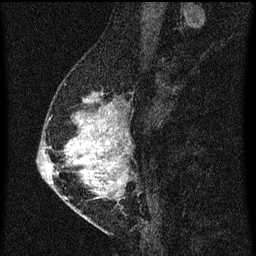
Breast MRI (dynamic contrast-enhanced), one sagittal slice. Dynamic contrast-enhanced series, image 2 of 3 at this slice position (ordered by acquisition). 1.5 T. TE 4.2 ms, TR 8 ms. 2 mm slice thickness. 256 × 256 image matrix, field of view 180 × 180 mm. Female patient, age 47 years.
Annotated regions visible in this slice (semi-automatically segmented with operator editing):
- analysis volume of interest (the breast-tissue region the enhancement analysis was run in; not a lesion): bounding box (x1, y1, x2, y2) in pixels: (50, 82, 139, 203)
- tumour enhancement mask (voxels above the 70 % enhancement threshold inside the analysis volume of interest): (67, 94, 129, 199)